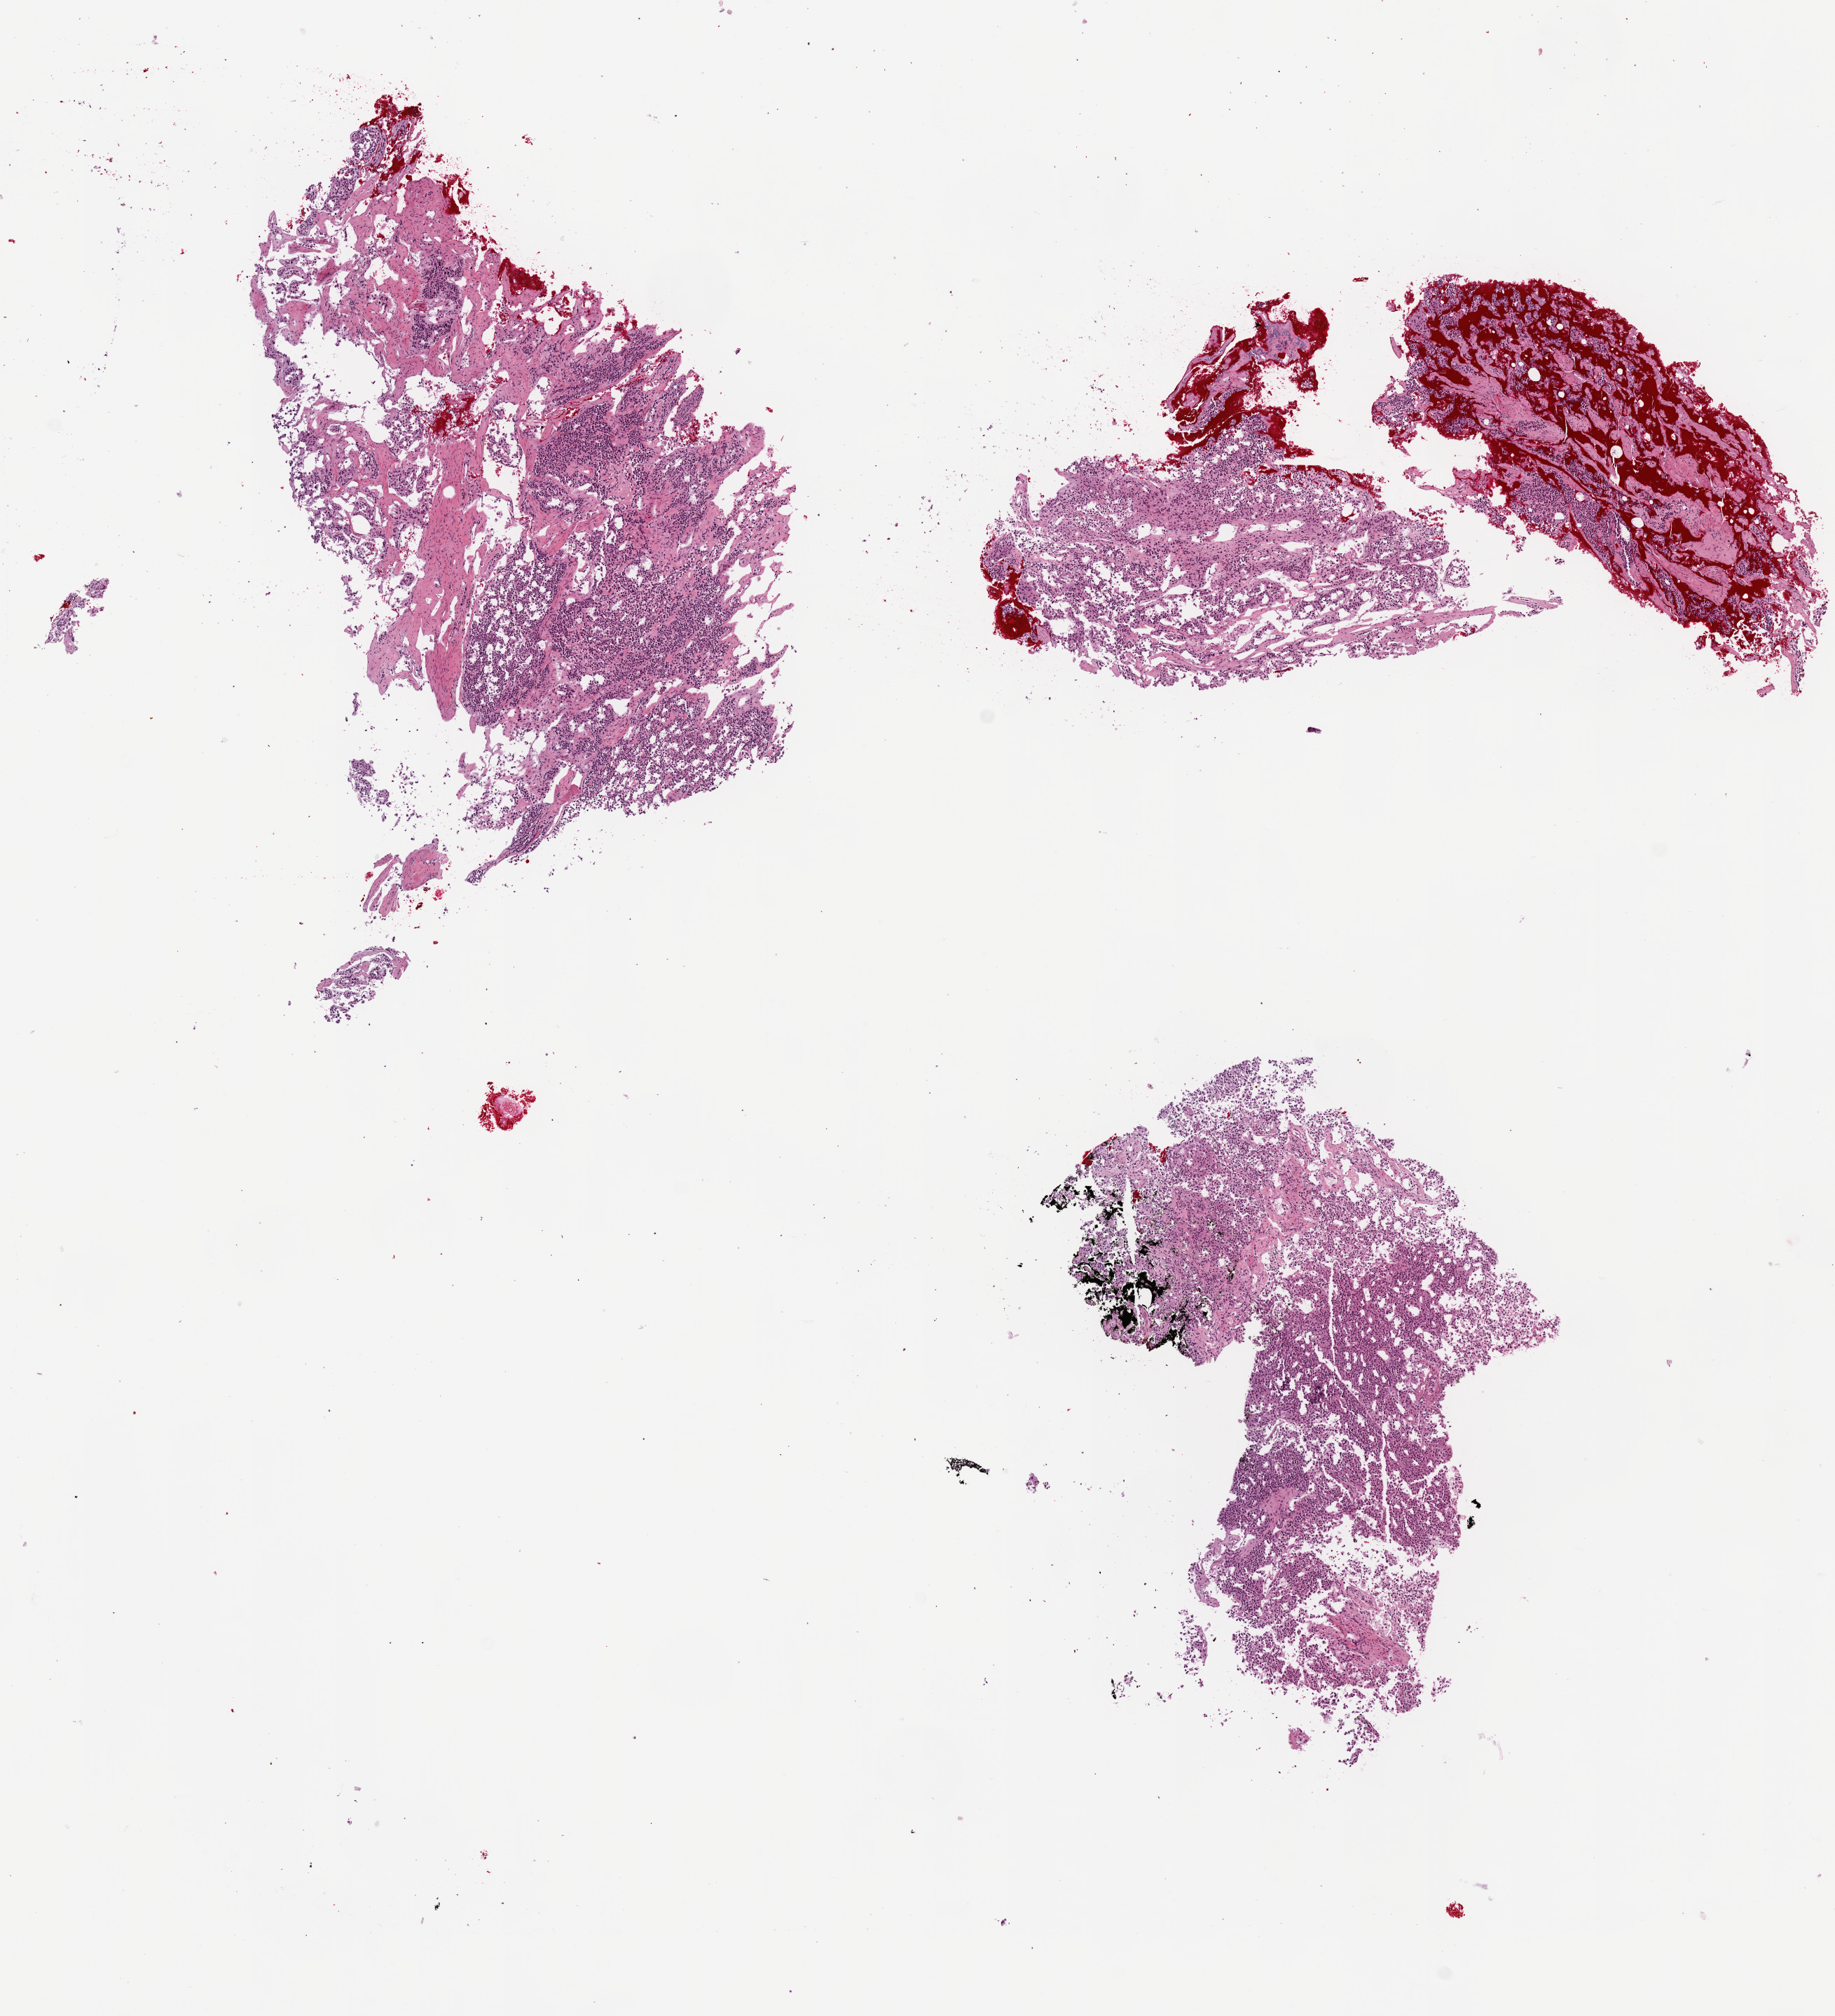
Digitized H&E tissue section (whole slide), whole scanned area (about 10.6 x 11.6 mm) shown as a low-resolution overview, frozen section from the top of the tissue portion, primary tumour sample from the adrenal cortex. Patient: female, age at initial diagnosis 59 years. Composition of this section per pathologist review: tumour cells 80%, tumour nuclei 90%, normal cells 0%, stromal cells 20%, necrosis 0%. Inflammatory infiltration, as recorded: lymphocyte infiltration 0%, monocyte infiltration 0%, neutrophil infiltration 0%.
Histologic diagnosis: Adrenal cortical carcinoma (cortex of adrenal gland). Laterality: right.